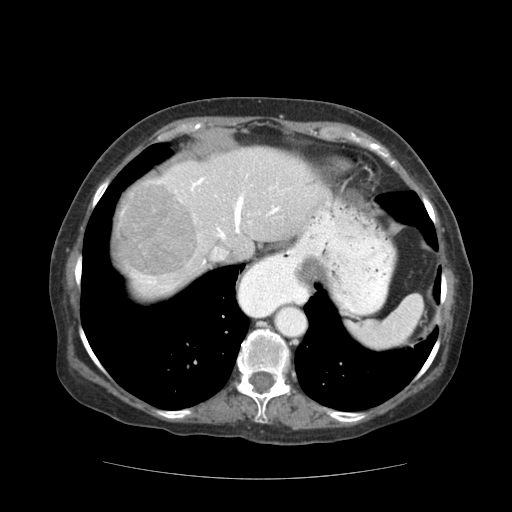
Contrast-enhanced abdominal CT (liver protocol), one axial slice. Position 93 of 111 along the scan axis. Reconstruction kernel STANDARD. Soft-tissue window (W 400 / L 40 HU). 2.5 mm slice thickness. 512 × 512 image matrix. From the clinical record (not read from this slice): diagnosis: hepatocellular carcinoma (patient treated with transarterial chemoembolisation; whether this scan precedes or follows treatment is not stated here); TNM stage (as recorded): Stage-I; Child-Pugh class: A; tumour size: 7.3 cm.
Annotated regions visible in this slice (semi-automatically segmented with operator editing):
- abdominal aorta: bounding box [x1, y1, x2, y2] px = [276, 307, 305, 336]
- liver parenchyma outside the tumour (the mass and vessels are separate outlines, so this box may not span the whole liver): [114, 146, 328, 296]
- mass: [120, 188, 196, 277]
- liver vessels: [141, 174, 280, 288]